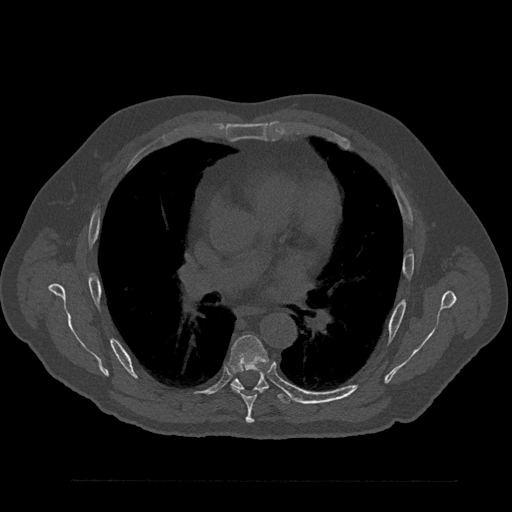
CT including the spine, one axial slice; position 535 of 797 along the scan axis; bone window (W 1800 / L 400 HU); 0.5 mm slice thickness; 512 × 512 image matrix. Male patient, age 61 years. From the clinical record (not read from this slice): primary cancer: prostate.
Structures marked on this image (semi-automatic segmentation, software-assisted and operator-edited):
- T6 vertebra: bounding box (x1, y1, x2, y2) in pixels: (228, 335, 269, 424)
- T7 vertebra: (231, 370, 293, 404)